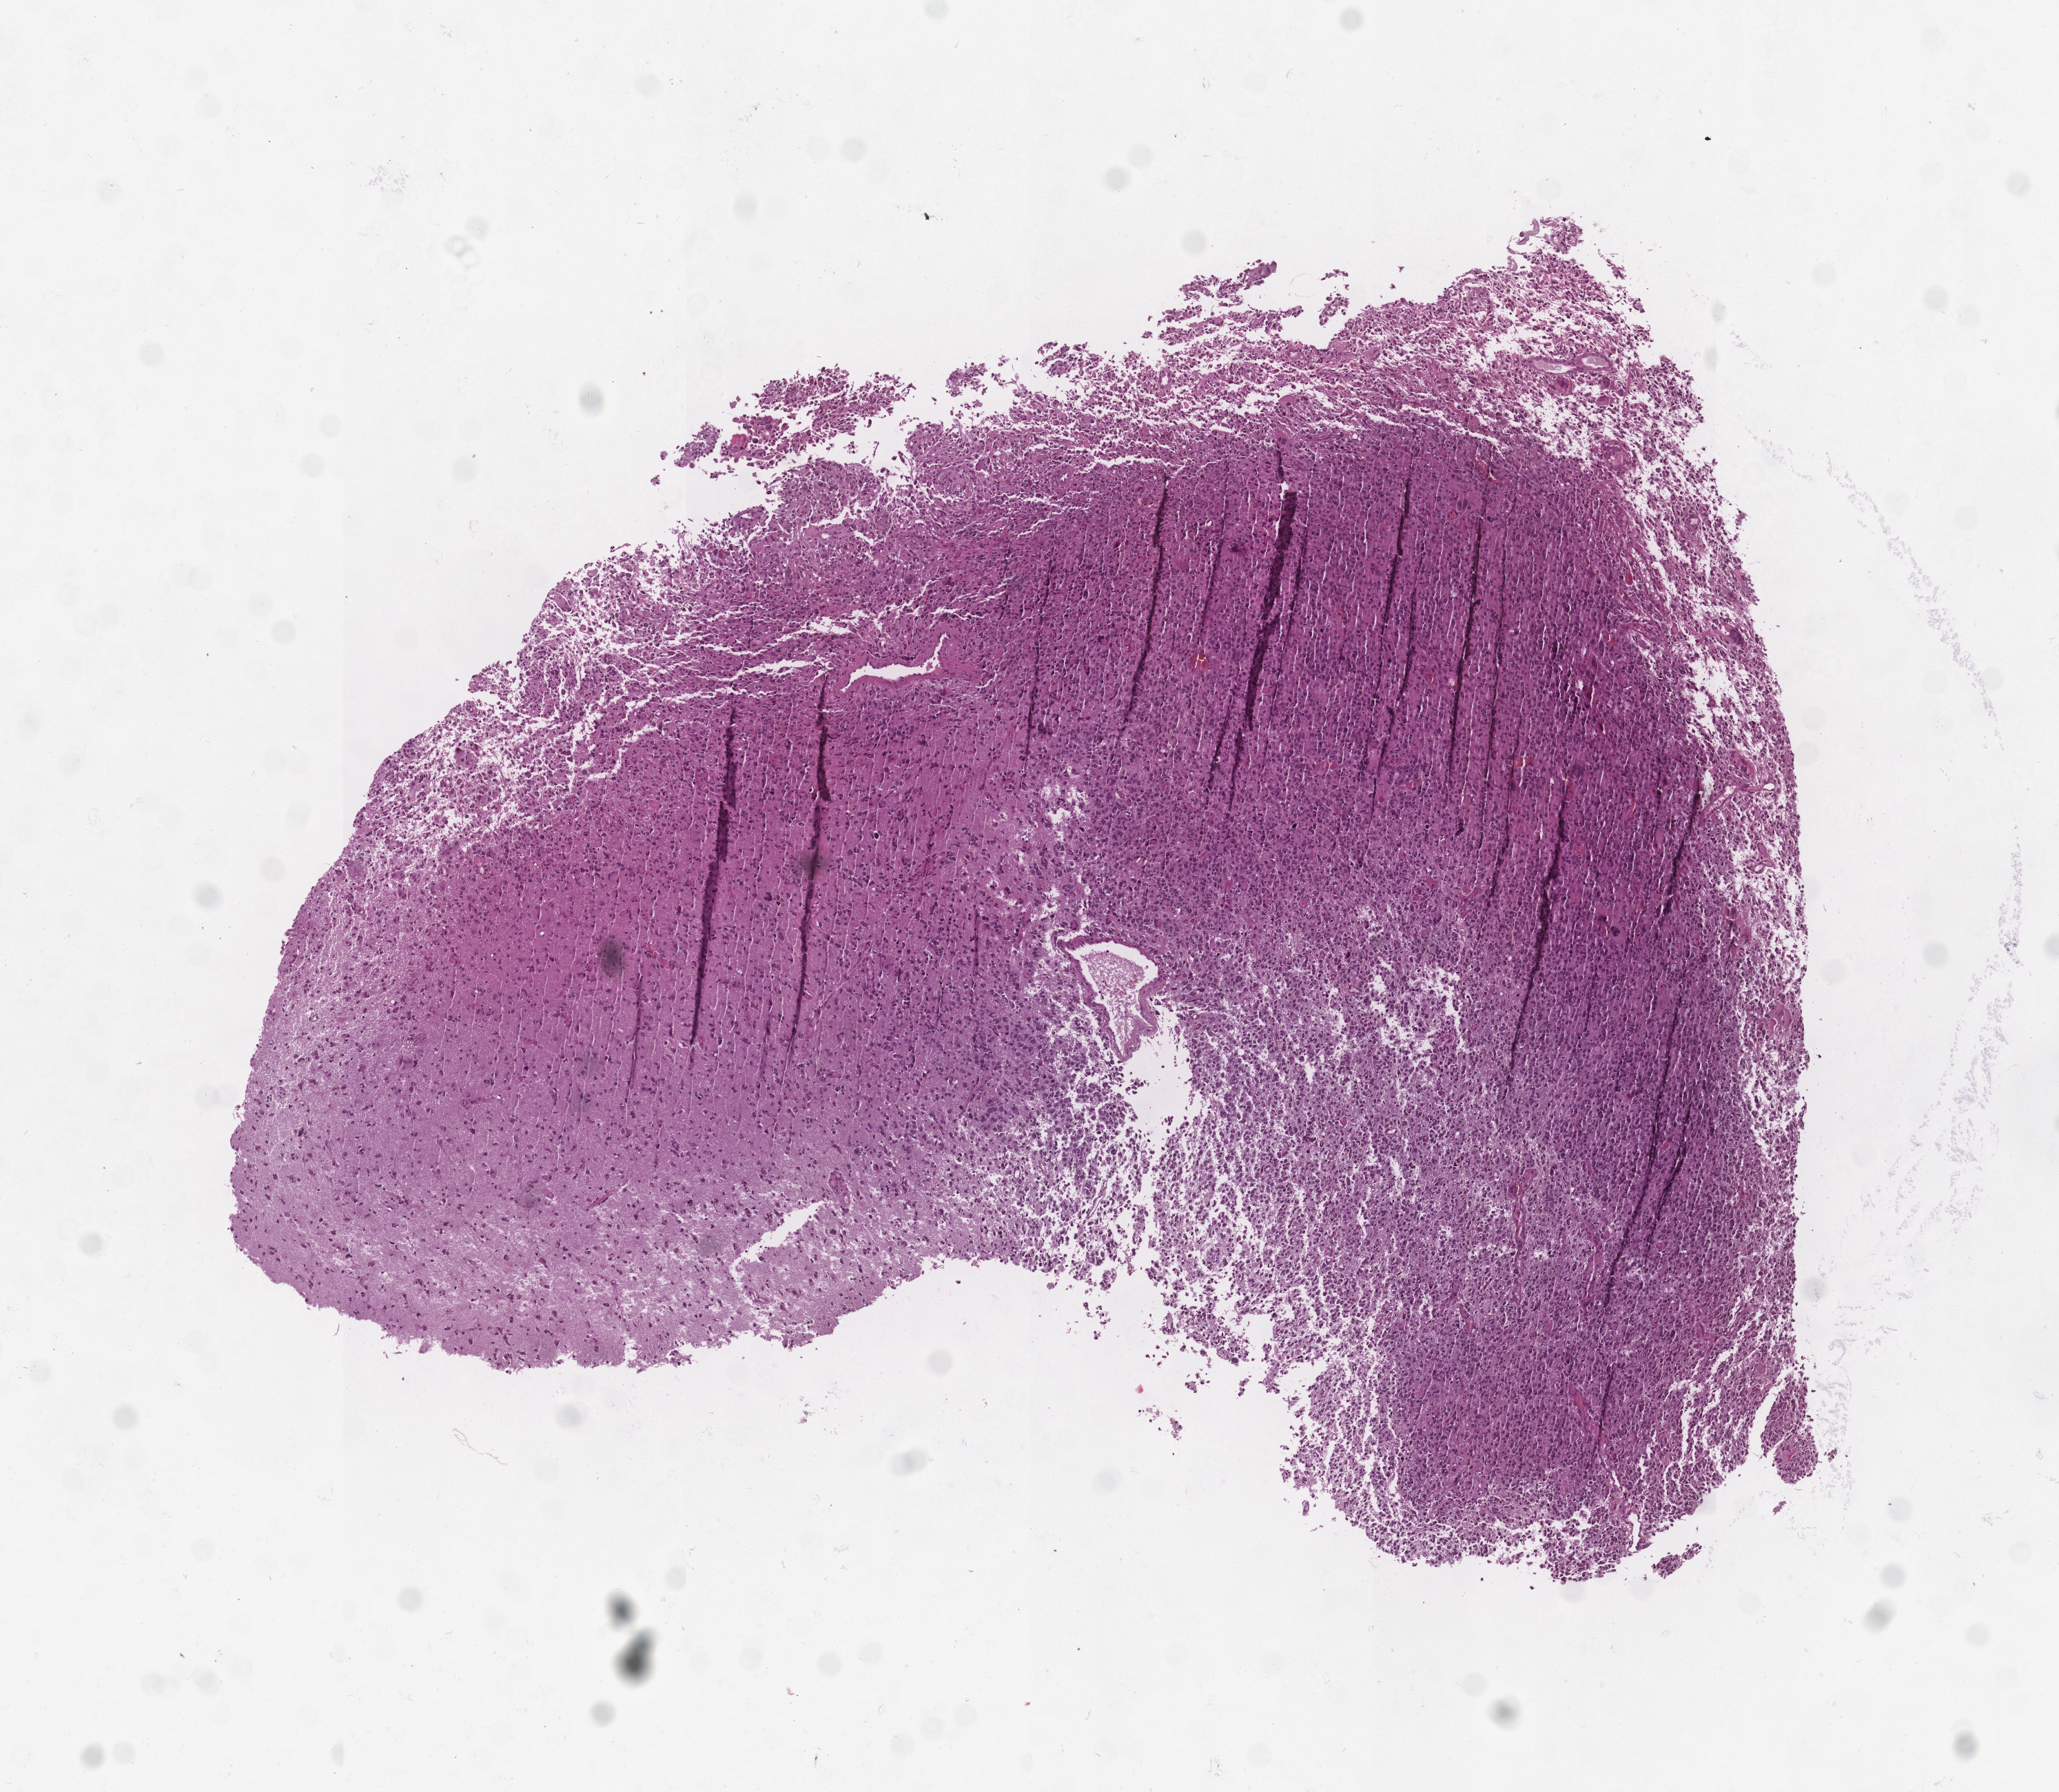
H&E whole-slide image — whole scanned area (about 6.0 x 5.2 mm) shown as a low-resolution overview, brain, tumour tissue. 59-year-old male patient.
• histologic diagnosis: Glioblastoma
• primary tumour site (as recorded): temporal lobe